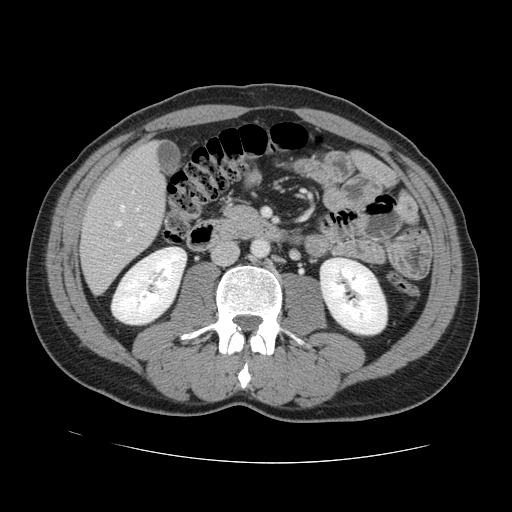
Contrast-enhanced abdominal CT, one axial slice. Position 39 of 131 along the scan axis. 120 kVp. Intravenous contrast given. Soft-tissue window (W 400 / L 40 HU). 2.5 mm slice thickness. 512 × 512 image matrix, field of view 380 × 380 mm. Male patient, age 40 years. Case-level facts recorded for this patient, not image findings: diagnosis: colorectal cancer liver metastases, imaged before liver resection; multiple liver metastases: yes; largest metastasis: 2.9 cm.
Outlined on this slice (outlined manually by an expert reader):
- hepatic veins: box from (x=116, y=205) to (x=142, y=226) px
- liver: (x=82, y=145)–(x=165, y=292)
- planned liver remnant (the part of the liver to remain after resection): (x=135, y=145)–(x=156, y=163)
- portal vein (with intrahepatic branches): (x=127, y=192)–(x=134, y=241)